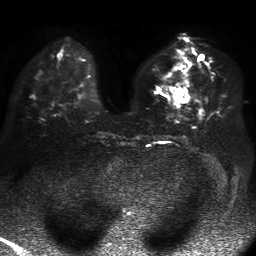
Breast MRI, one axial slice. Diffusion-weighted series; image 2 of 4 stored at this slice position (different b-values; order by instance number). 1.5 T. 4 mm slice thickness. 256 × 256 image matrix, field of view 360 × 360 mm. Female patient.
Structures marked on this image (outlined manually by an expert reader):
- tumour on diffusion-weighted imaging: bounding box (x1, y1, x2, y2) in pixels: (174, 88, 189, 103)